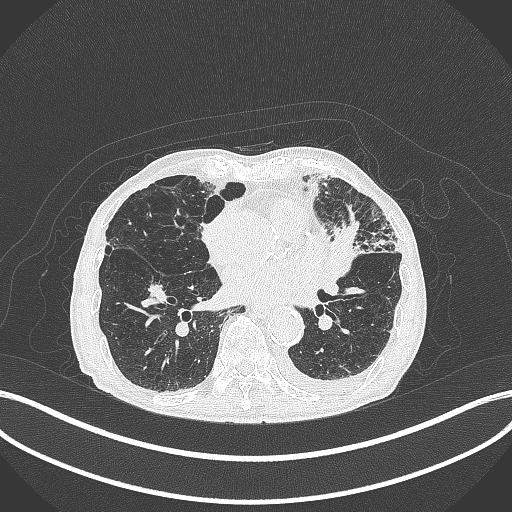
Chest CT, one axial slice; slice 159 of 385 in the series (ordered by position); 120 kVp; lung window (W 1500 / L -600 HU); 512 × 512 image matrix, field of view 400 × 400 mm. Male patient, age 90 years or older. Case-level facts recorded for this patient, not image findings: clinical TNM (as recorded): T2b N1 M0.
Outlined on this slice (bounding box drawn by a radiologist):
- lung tumour (recorded histology: squamous cell carcinoma): box from (x=331, y=219) to (x=358, y=278) px